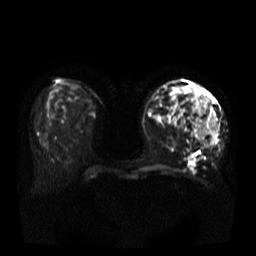
Breast MRI, one axial slice. Slice 15 of 37 in the series (ordered by position). Diffusion-weighted series; image 2 of 4 stored at this slice position (different b-values; order by instance number). 3 T. 256 × 256 image matrix, field of view 380 × 380 mm. Female patient.
Outlined on this slice (expert manual segmentation):
- tumour on diffusion-weighted imaging: box from (x=193, y=97) to (x=217, y=147) px